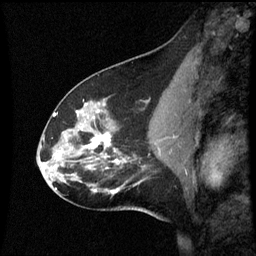
Breast MRI (dynamic contrast-enhanced), one sagittal slice; slice 29 of 60 in the series (ordered by position); dynamic contrast-enhanced series, image 2 of 3 at this slice position (ordered by acquisition); 1.5 T; TE 4.2 ms, TR 8.9 ms; 2 mm slice thickness; 256 × 256 image matrix, field of view 200 × 200 mm. Female patient, age 45 years. Case-level facts recorded for this patient, not image findings: setting: breast cancer imaged before/during neoadjuvant chemotherapy; receptor status: HR-positive, HER2-negative.
Outlined on this slice (semi-automatic segmentation, software-assisted and operator-edited):
- analysis volume of interest (the breast-tissue region the enhancement analysis was run in; not a lesion): box from (x=46, y=94) to (x=171, y=205) px
- tumour enhancement mask (voxels above the 70 % enhancement threshold inside the analysis volume of interest): (x=86, y=104)–(x=125, y=163)